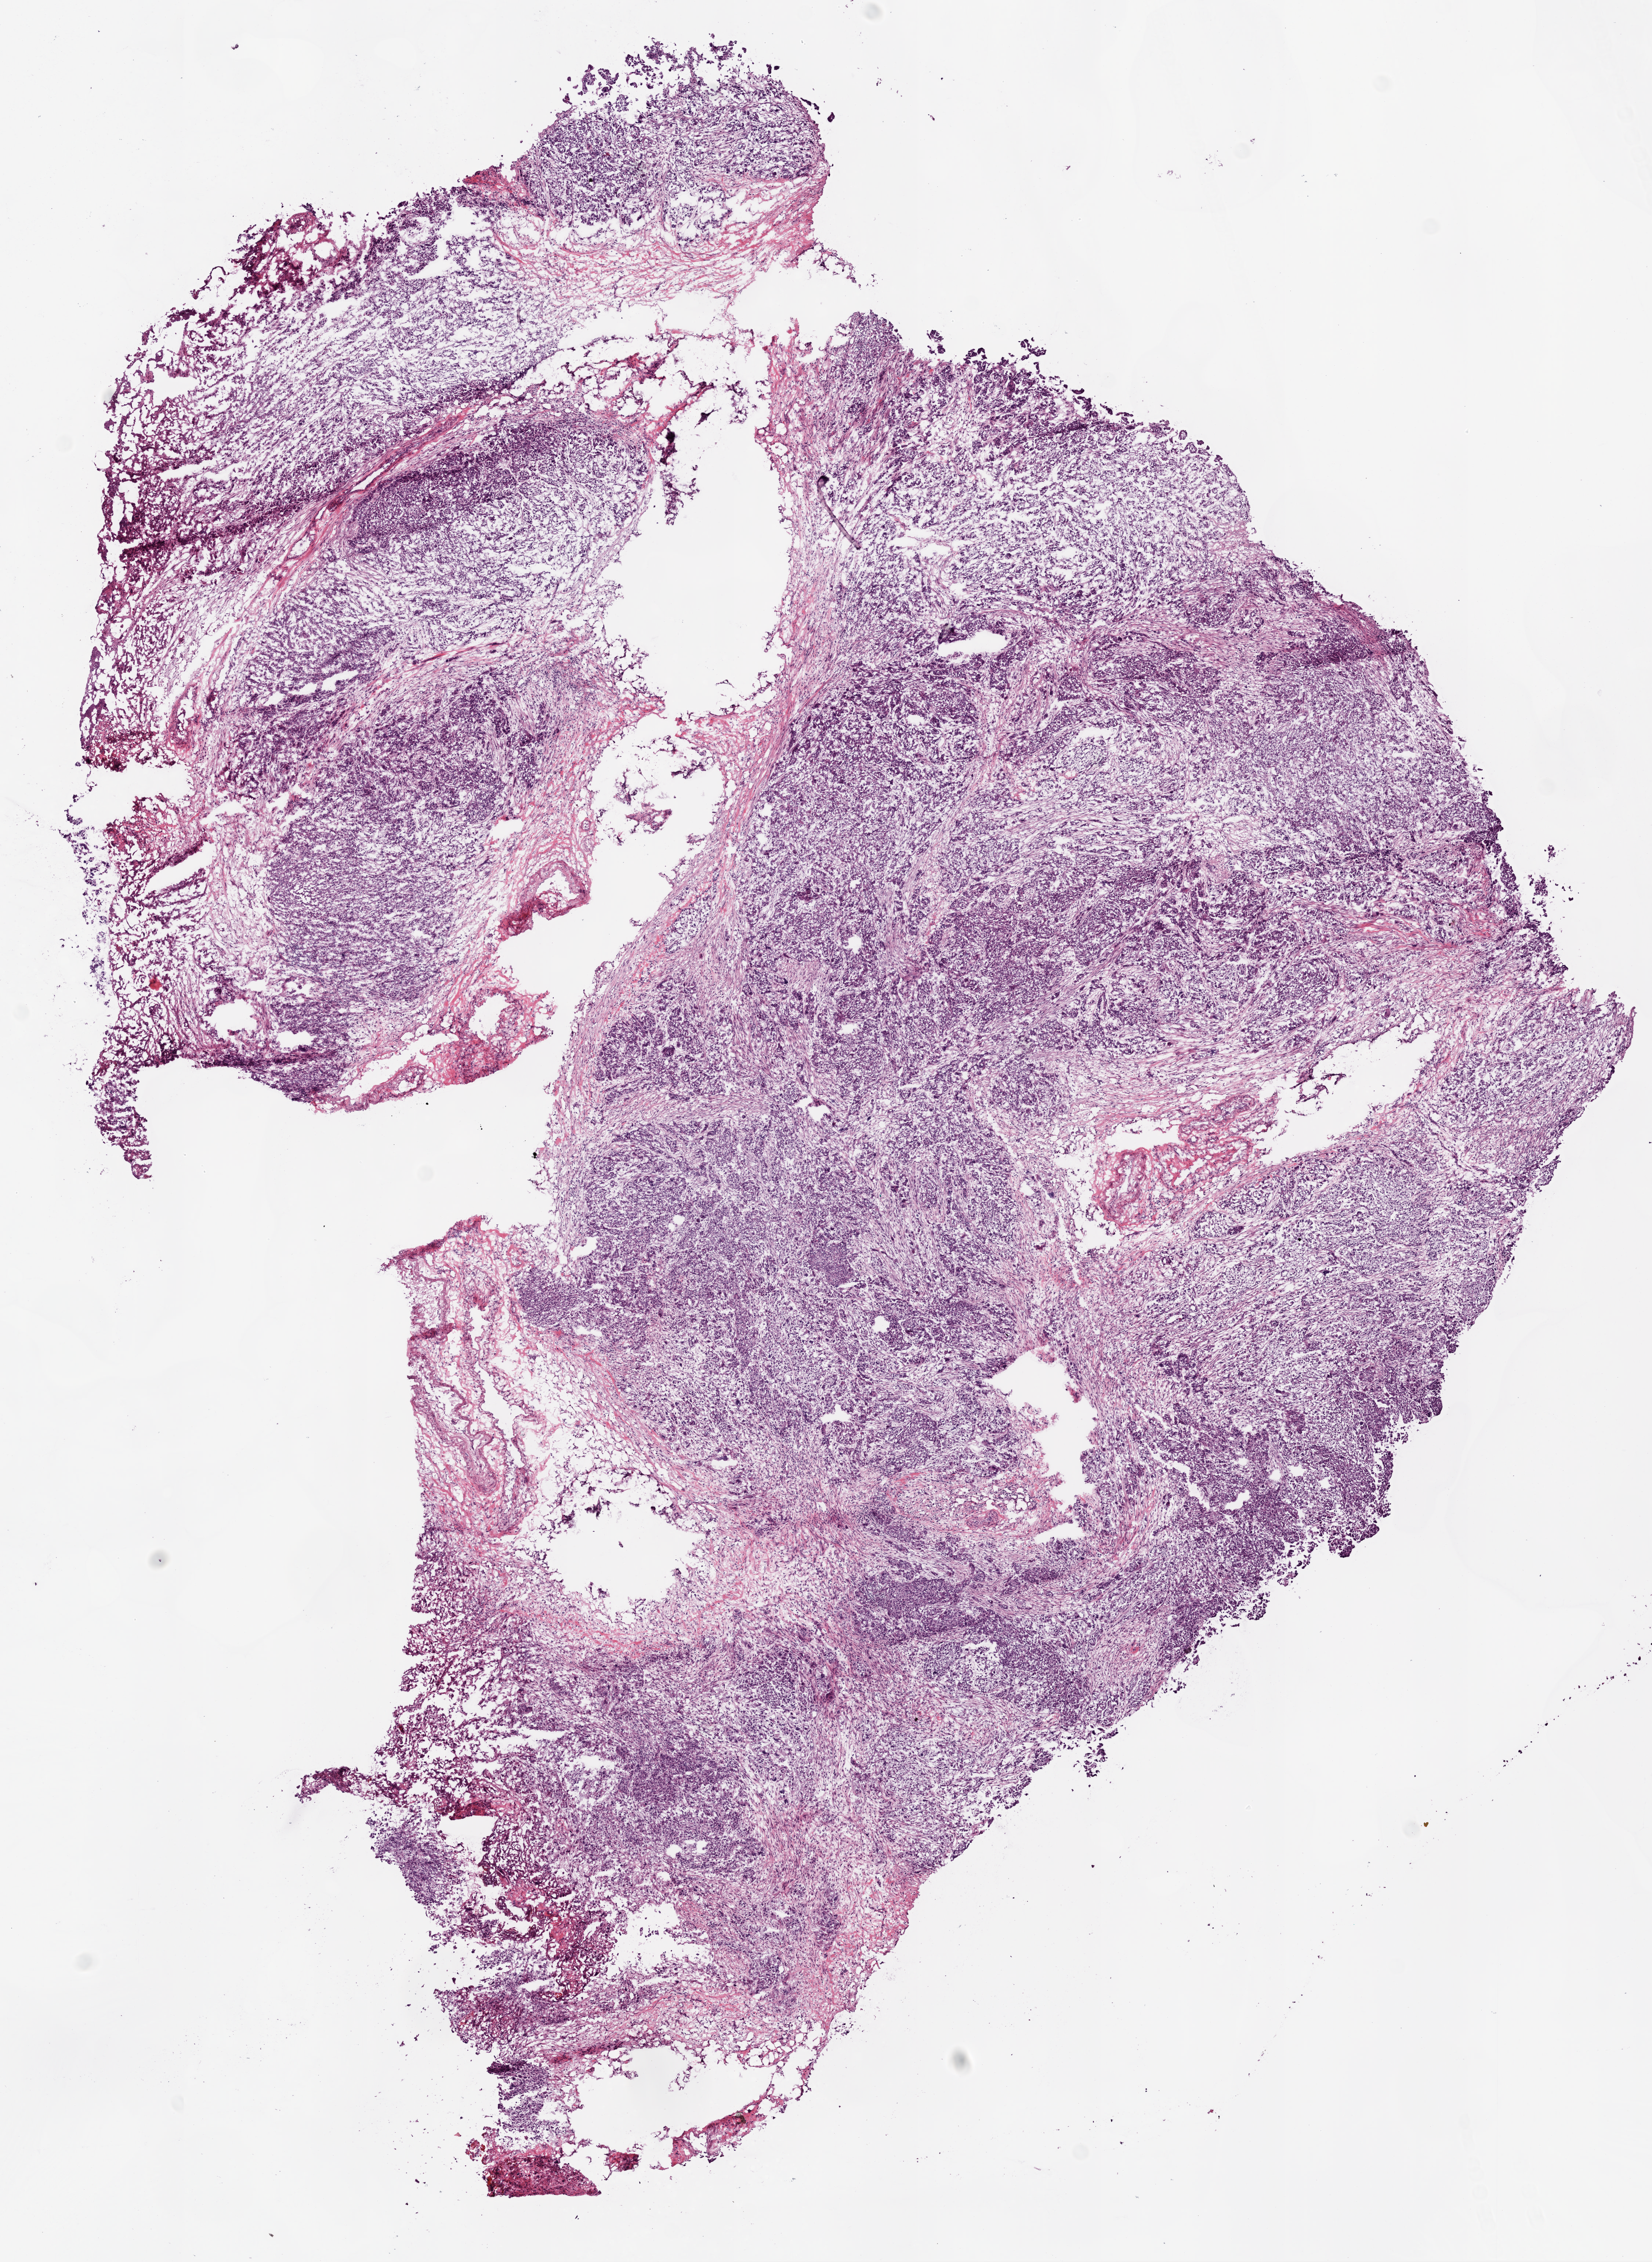
Digitized H&E-stained tissue section (whole slide), low-resolution overview of the scanned area, about 9.0 x 12.4 mm; frozen section; primary tumour sample from the ovary. Female, age 64 years at initial diagnosis. Histologic grade: G3 (poorly differentiated). Slide review estimates, as recorded: tumour cells 85%, tumour nuclei 90%, normal cells 0%, stromal cells 15%, necrosis 0%.
Laterality: right. FIGO stage: IV. Histologic diagnosis: Serous cystadenocarcinoma, NOS.